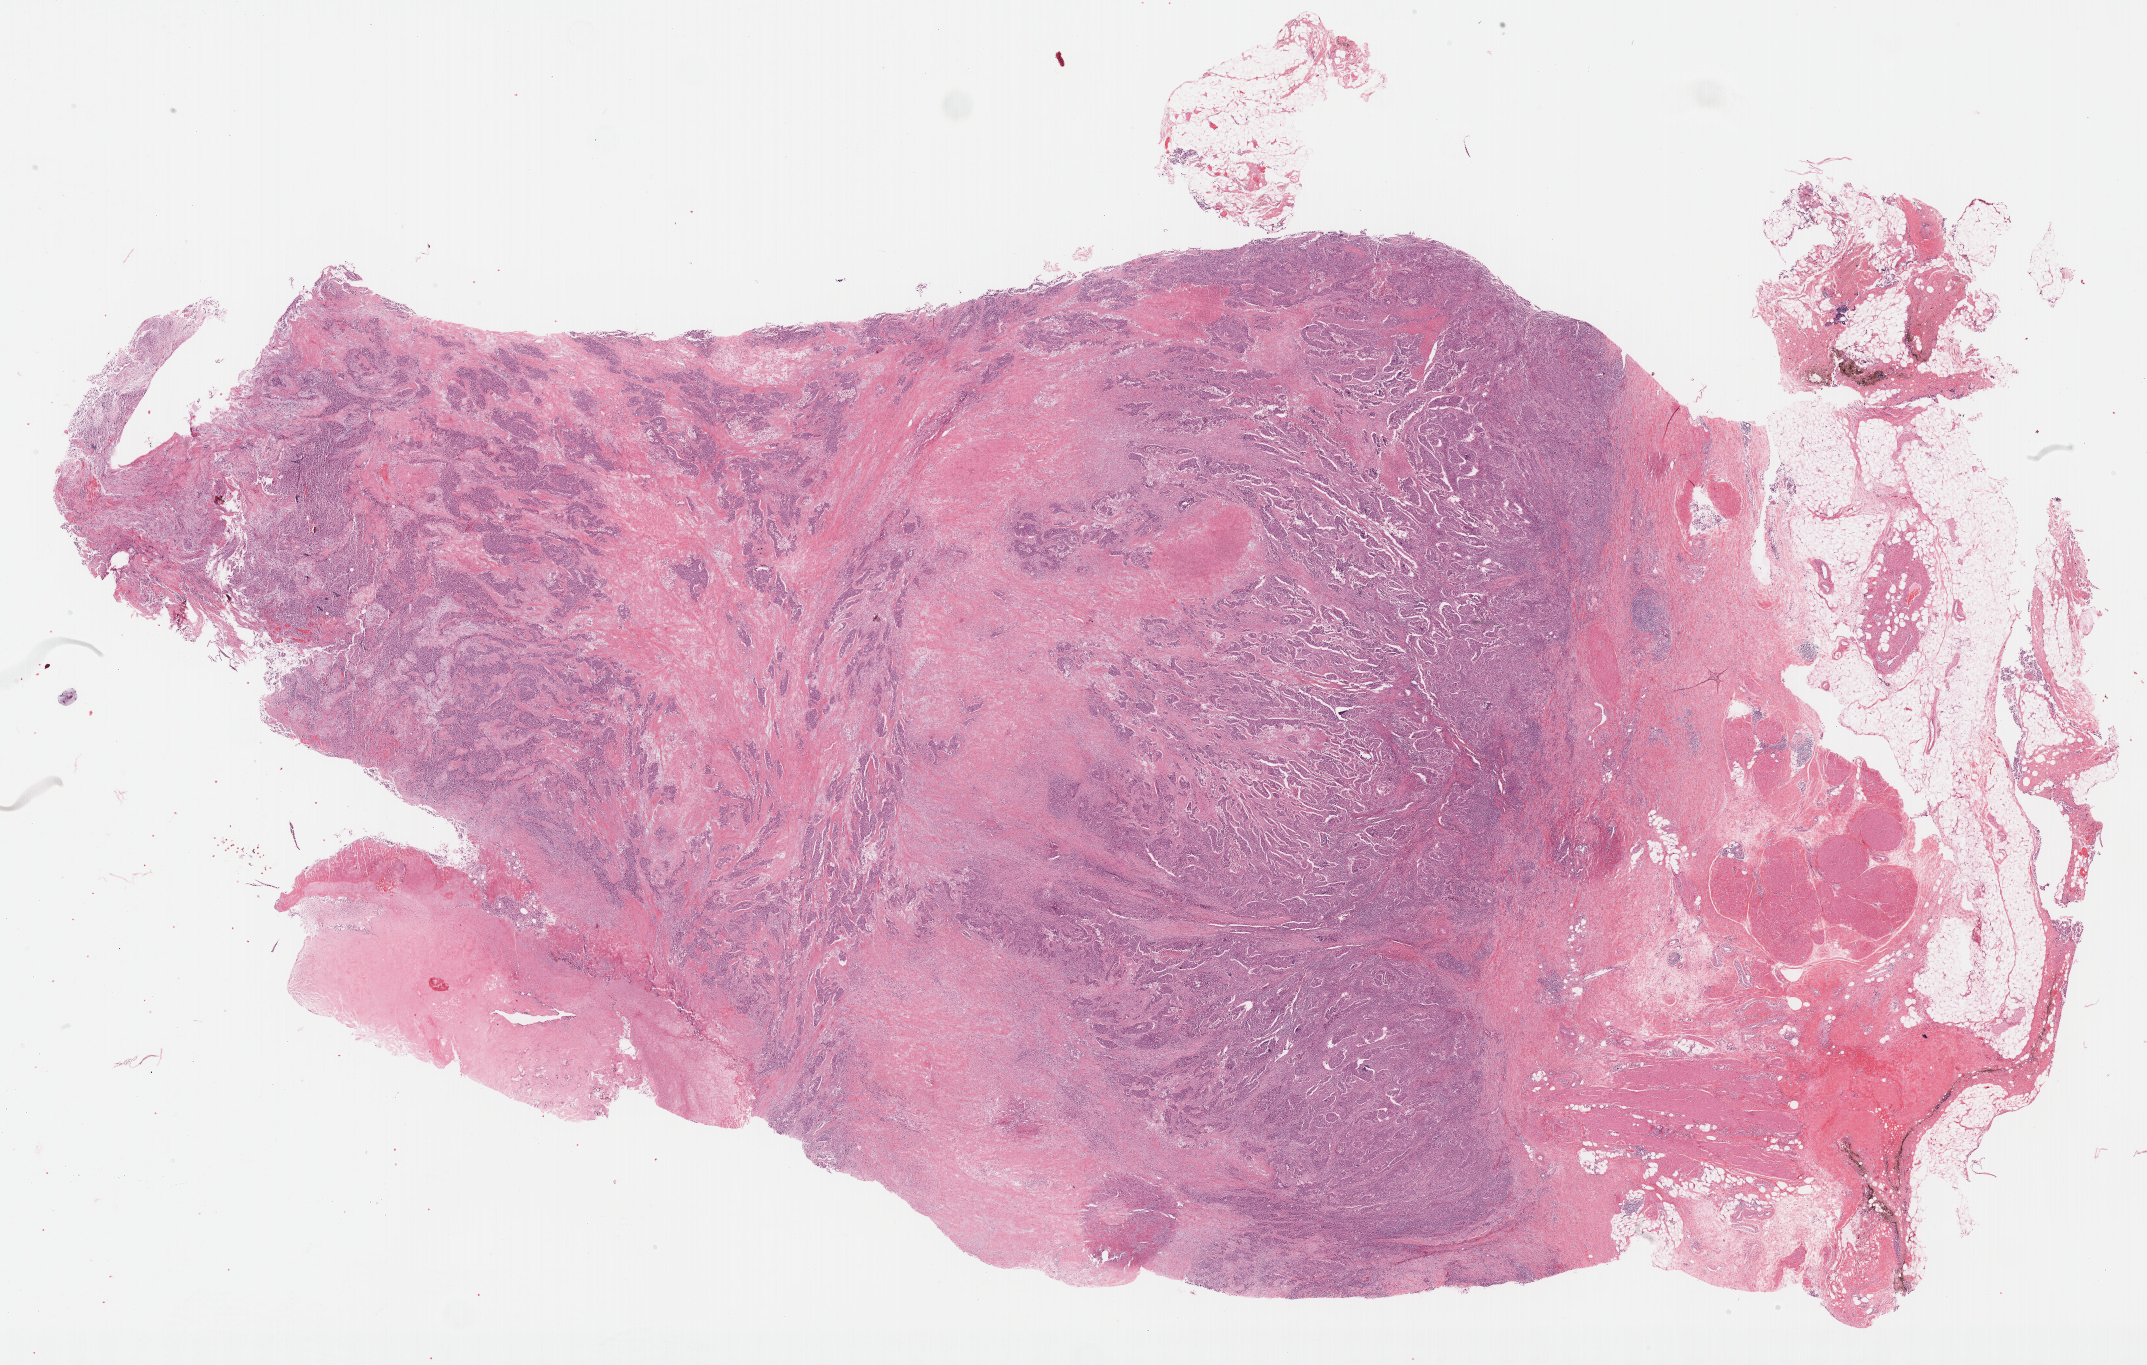
Hematoxylin and eosin (H&E) stained whole-slide image, a low-resolution overview of the entire scanned area, about 34.7 x 22.1 mm (from a 40x scan), formalin-fixed paraffin-embedded (FFPE) diagnostic section, sample: primary tumour, bladder. Patient: male, age at initial diagnosis 72 years. Histologic grade: high grade.
Diagnosis: Transitional cell carcinoma. AJCC pathologic stage: III (6th edition). Lymph nodes positive (case pathology): 0 of 22 examined.